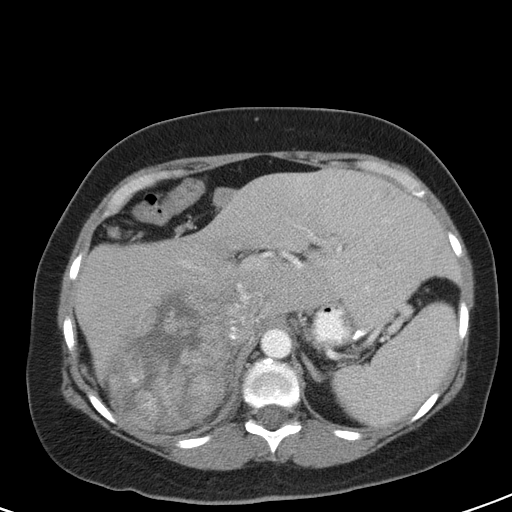
Contrast-enhanced abdominal CT, one axial slice; slice 76 of 126 in the series (ordered by position); 120 kVp; soft-tissue window (W 400 / L 40 HU); 5 mm slice thickness; 512 × 512 image matrix. Patient: female, 51 years. From the clinical record (not read from this slice): diagnosis: adrenocortical carcinoma; tumour side: right adrenal; tumour size at pathology: 17 cm.
Outlined on this slice (semi-automatically segmented with operator editing):
- mass: bounding box [x1, y1, x2, y2] px = [109, 288, 252, 430]